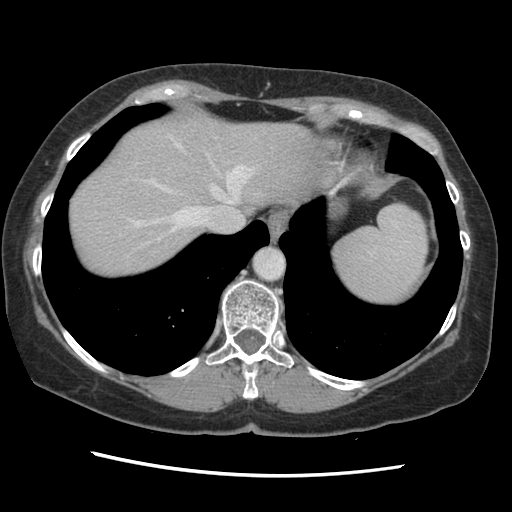
Contrast-enhanced abdominal CT, one axial slice; position 117 of 141 along the scan axis; 120 kVp; soft-tissue window (W 400 / L 40 HU); 2.5 mm slice thickness; 512 × 512 image matrix, field of view 330 × 330 mm. Female patient, age 61 years. Case-level facts recorded for this patient, not image findings: diagnosis: colorectal cancer liver metastases, imaged before liver resection; multiple liver metastases: no; largest metastasis: 2.4 cm; disease in both lobes: no.
Structures marked on this image (manually delineated by an expert):
- hepatic veins: bounding box <129,137,253,247> (left, top, right, bottom; pixels)
- liver: <68,114,318,279>
- planned liver remnant (the part of the liver to remain after resection): <68,113,327,279>